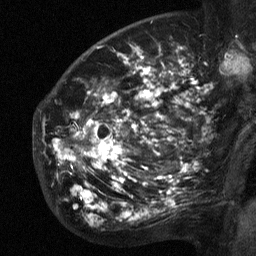
Breast MRI (dynamic contrast-enhanced), one sagittal slice; dynamic contrast-enhanced study with each time point stored as its own series, time point 2 of 3 at this slice position (early post-contrast, ordered by acquisition time); 1.5 T; TE 4.8 ms, TR 27 ms; 2.3 mm slice thickness; 256 × 256 image matrix, field of view 200 × 200 mm. Patient: female, 50 years. Case-level facts recorded for this patient, not image findings: setting: breast cancer imaged before/during neoadjuvant chemotherapy; receptor status: HER2-positive.
Outlined on this slice (semi-automatically segmented with operator editing):
- analysis volume of interest (the breast-tissue region the enhancement analysis was run in; not a lesion): box from (x=53, y=64) to (x=211, y=218) px
- tumour enhancement mask (voxels above the 90 % enhancement threshold inside the analysis volume of interest): (x=55, y=64)–(x=195, y=216)